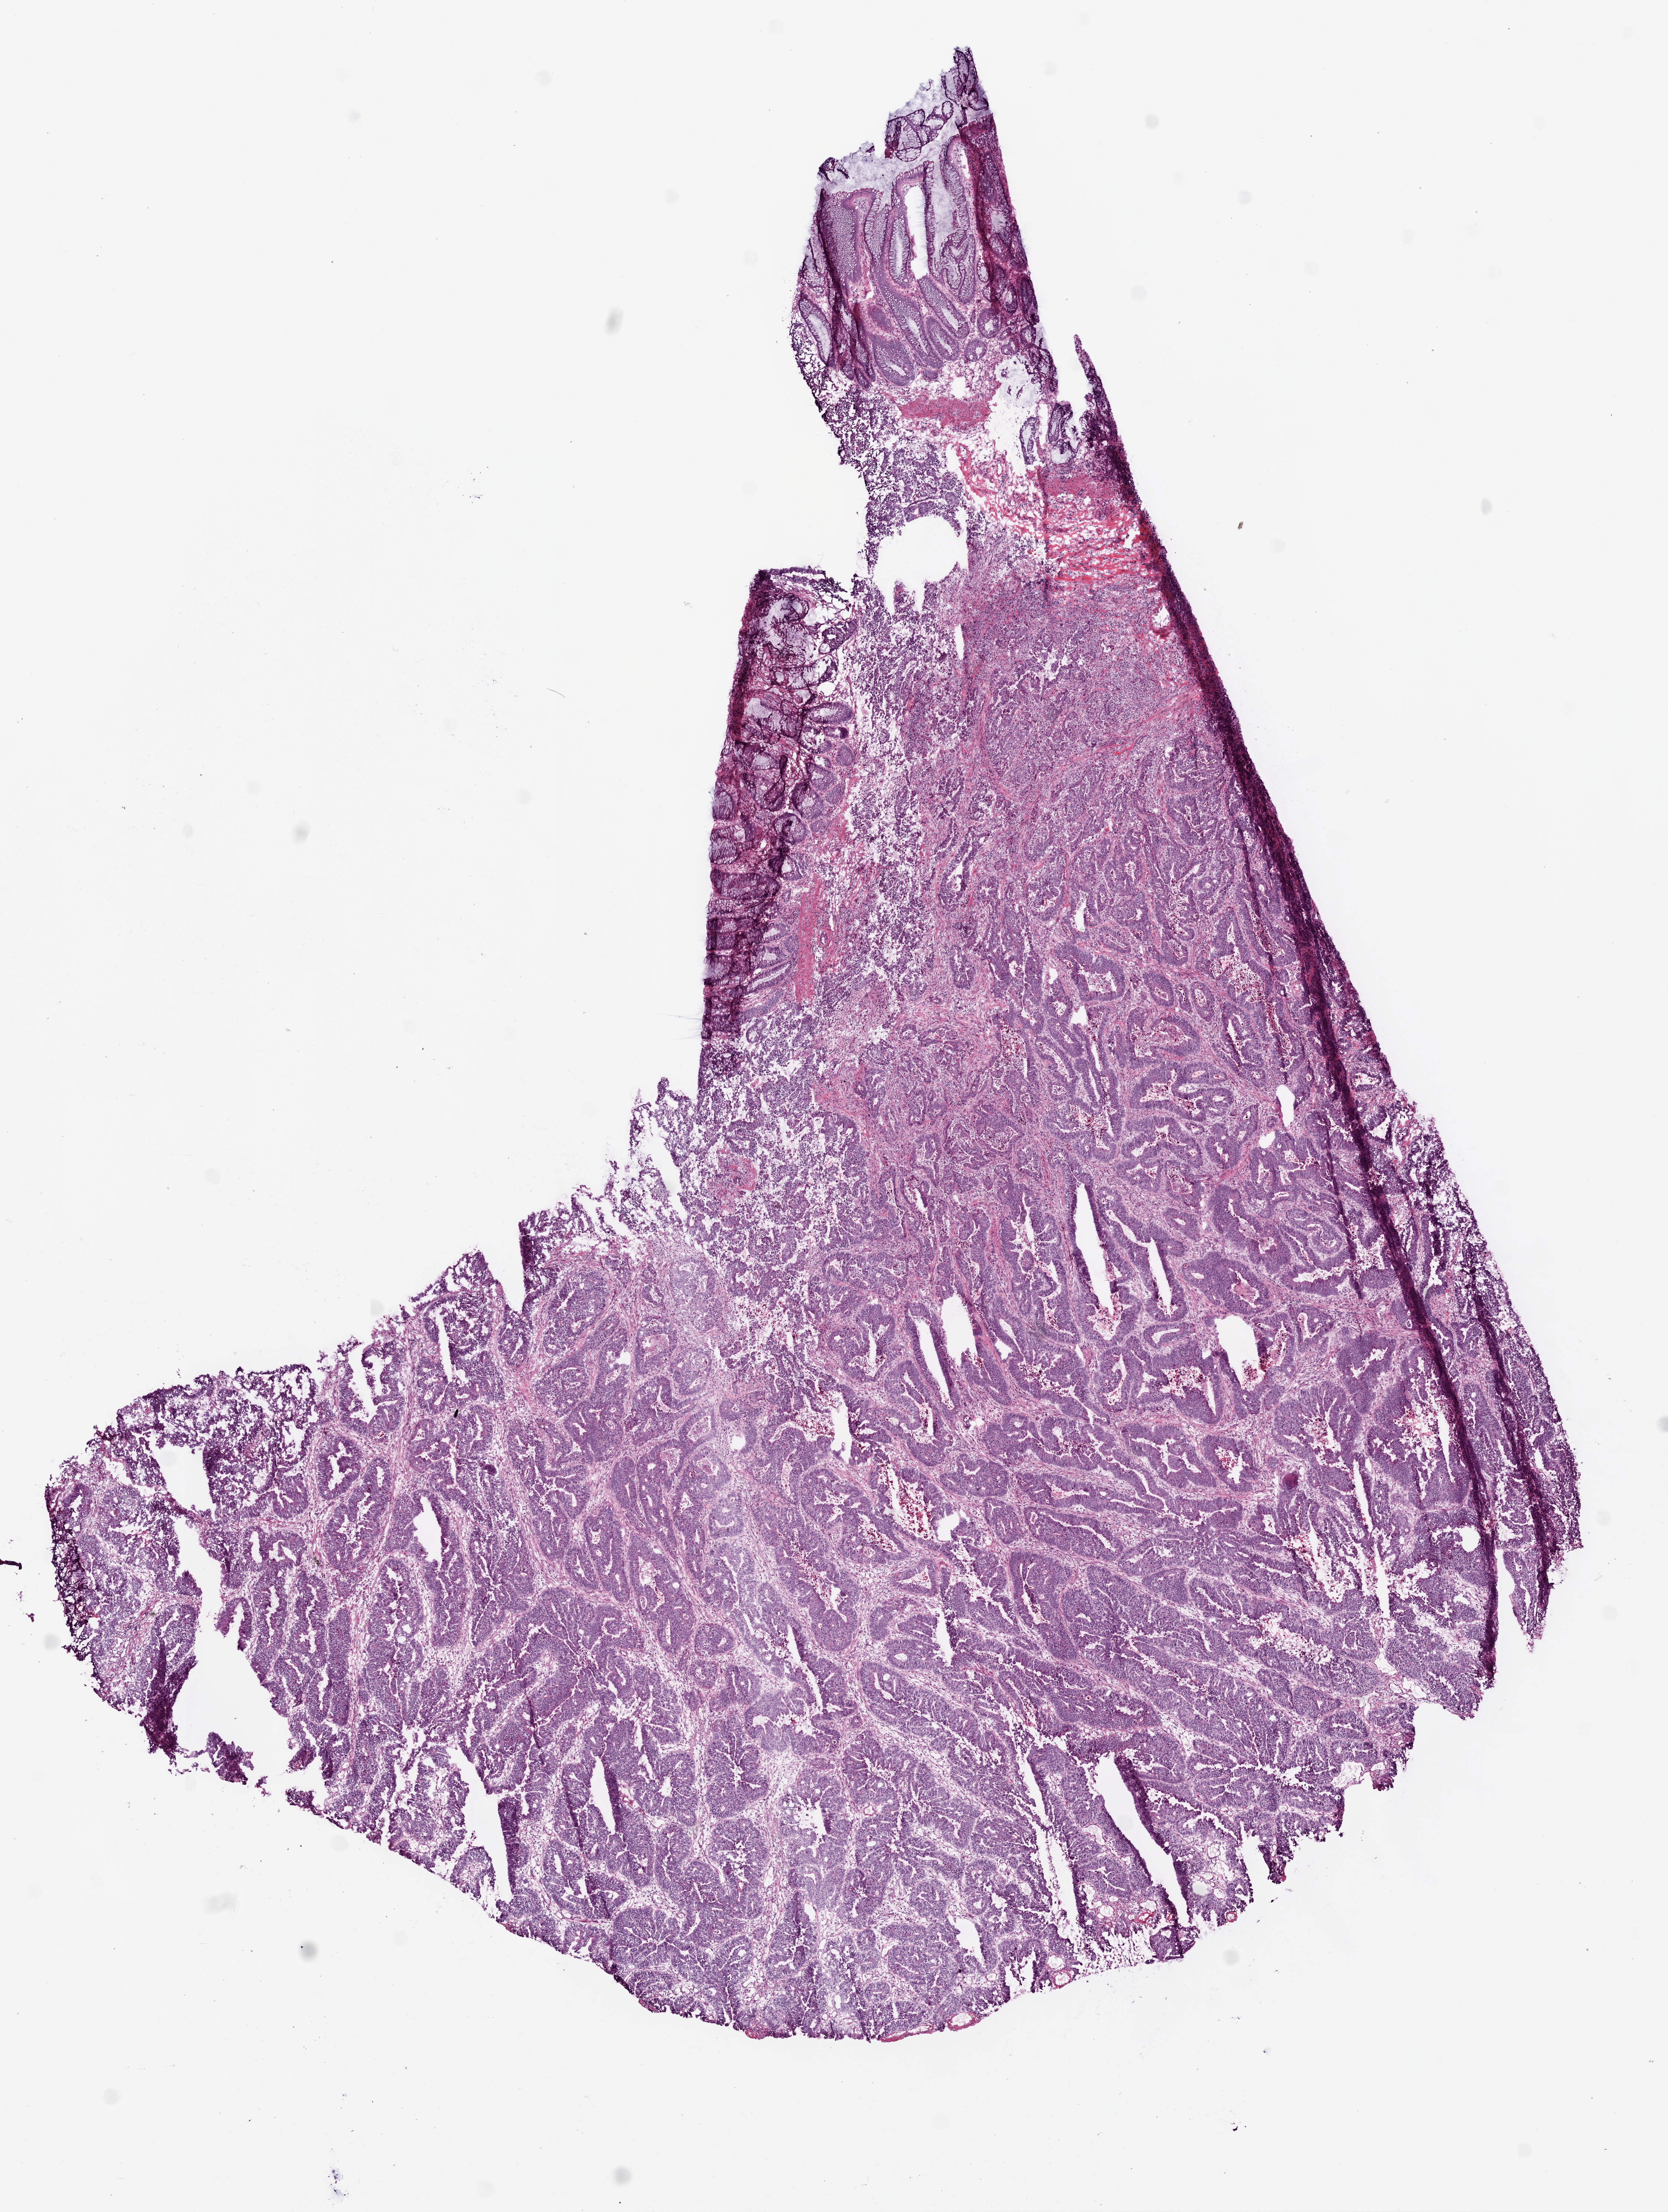
H&E-stained whole-slide image — shown as a low-resolution overview of the whole scanned area (about 9.0 x 12.0 mm). Frozen section. Primary tumour sample from the colon. Male, age 65 years at initial diagnosis. Composition of this section per pathologist review: tumour cells 90%, tumour nuclei 80%, normal cells 5%, necrosis 5%. Inflammatory infiltration, as recorded: lymphocyte infiltration 1%.
* AJCC pathologic stage: III
* pathologic diagnosis: Adenocarcinoma, NOS (descending colon)
* lymph nodes positive (case pathology): 12 of 18 examined
* TNM: T3 N2 M0